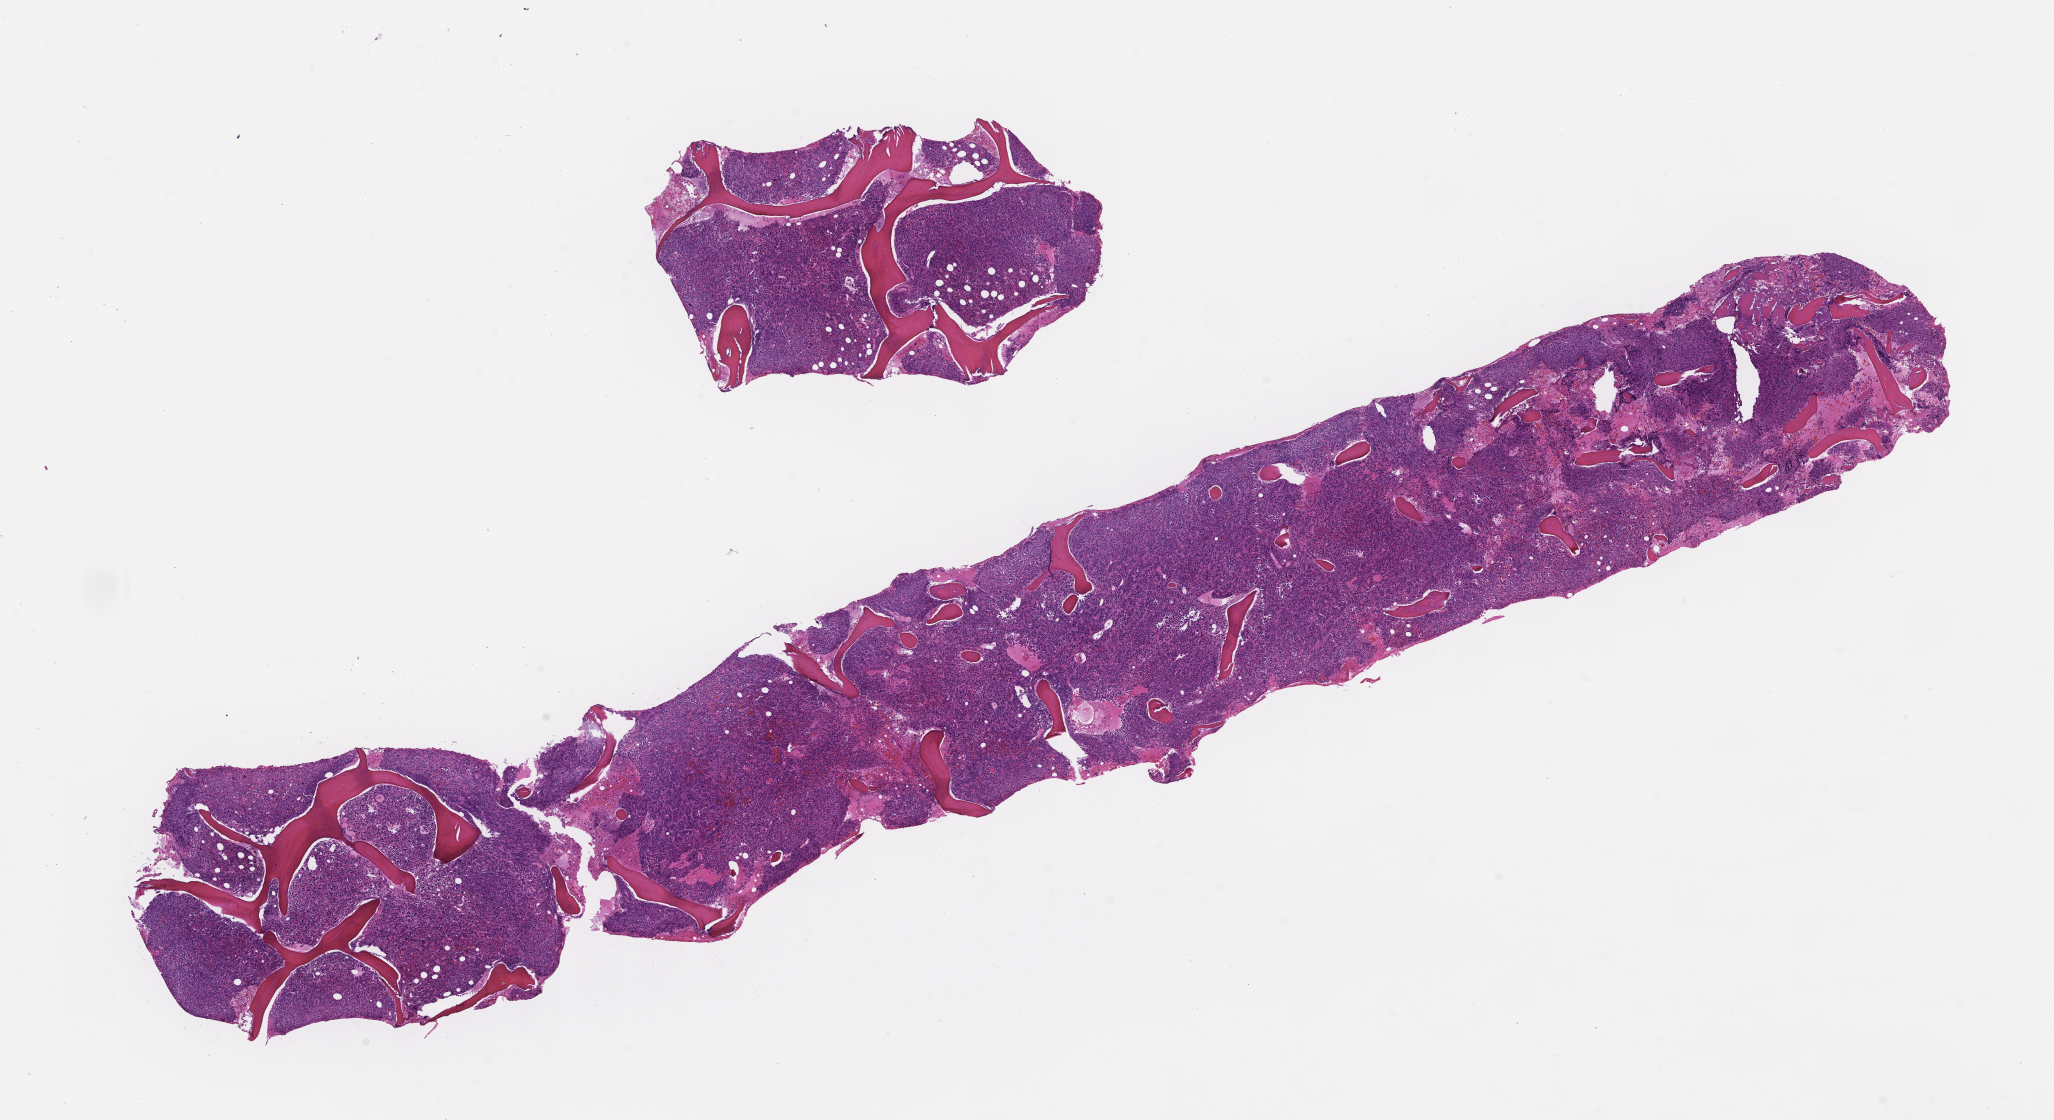
Whole-slide image, haematoxylin and eosin stain, shown as a low-resolution overview of the whole scanned area (about 16.6 x 9.0 mm). Formalin-fixed, paraffin-embedded (FFPE) tissue. Specimen time point: archival tissue. Patient sex: female.
This section: metastasis (sampled organ not recorded). Primary diagnosis of the patient: Small Cell Lung Carcinoma.